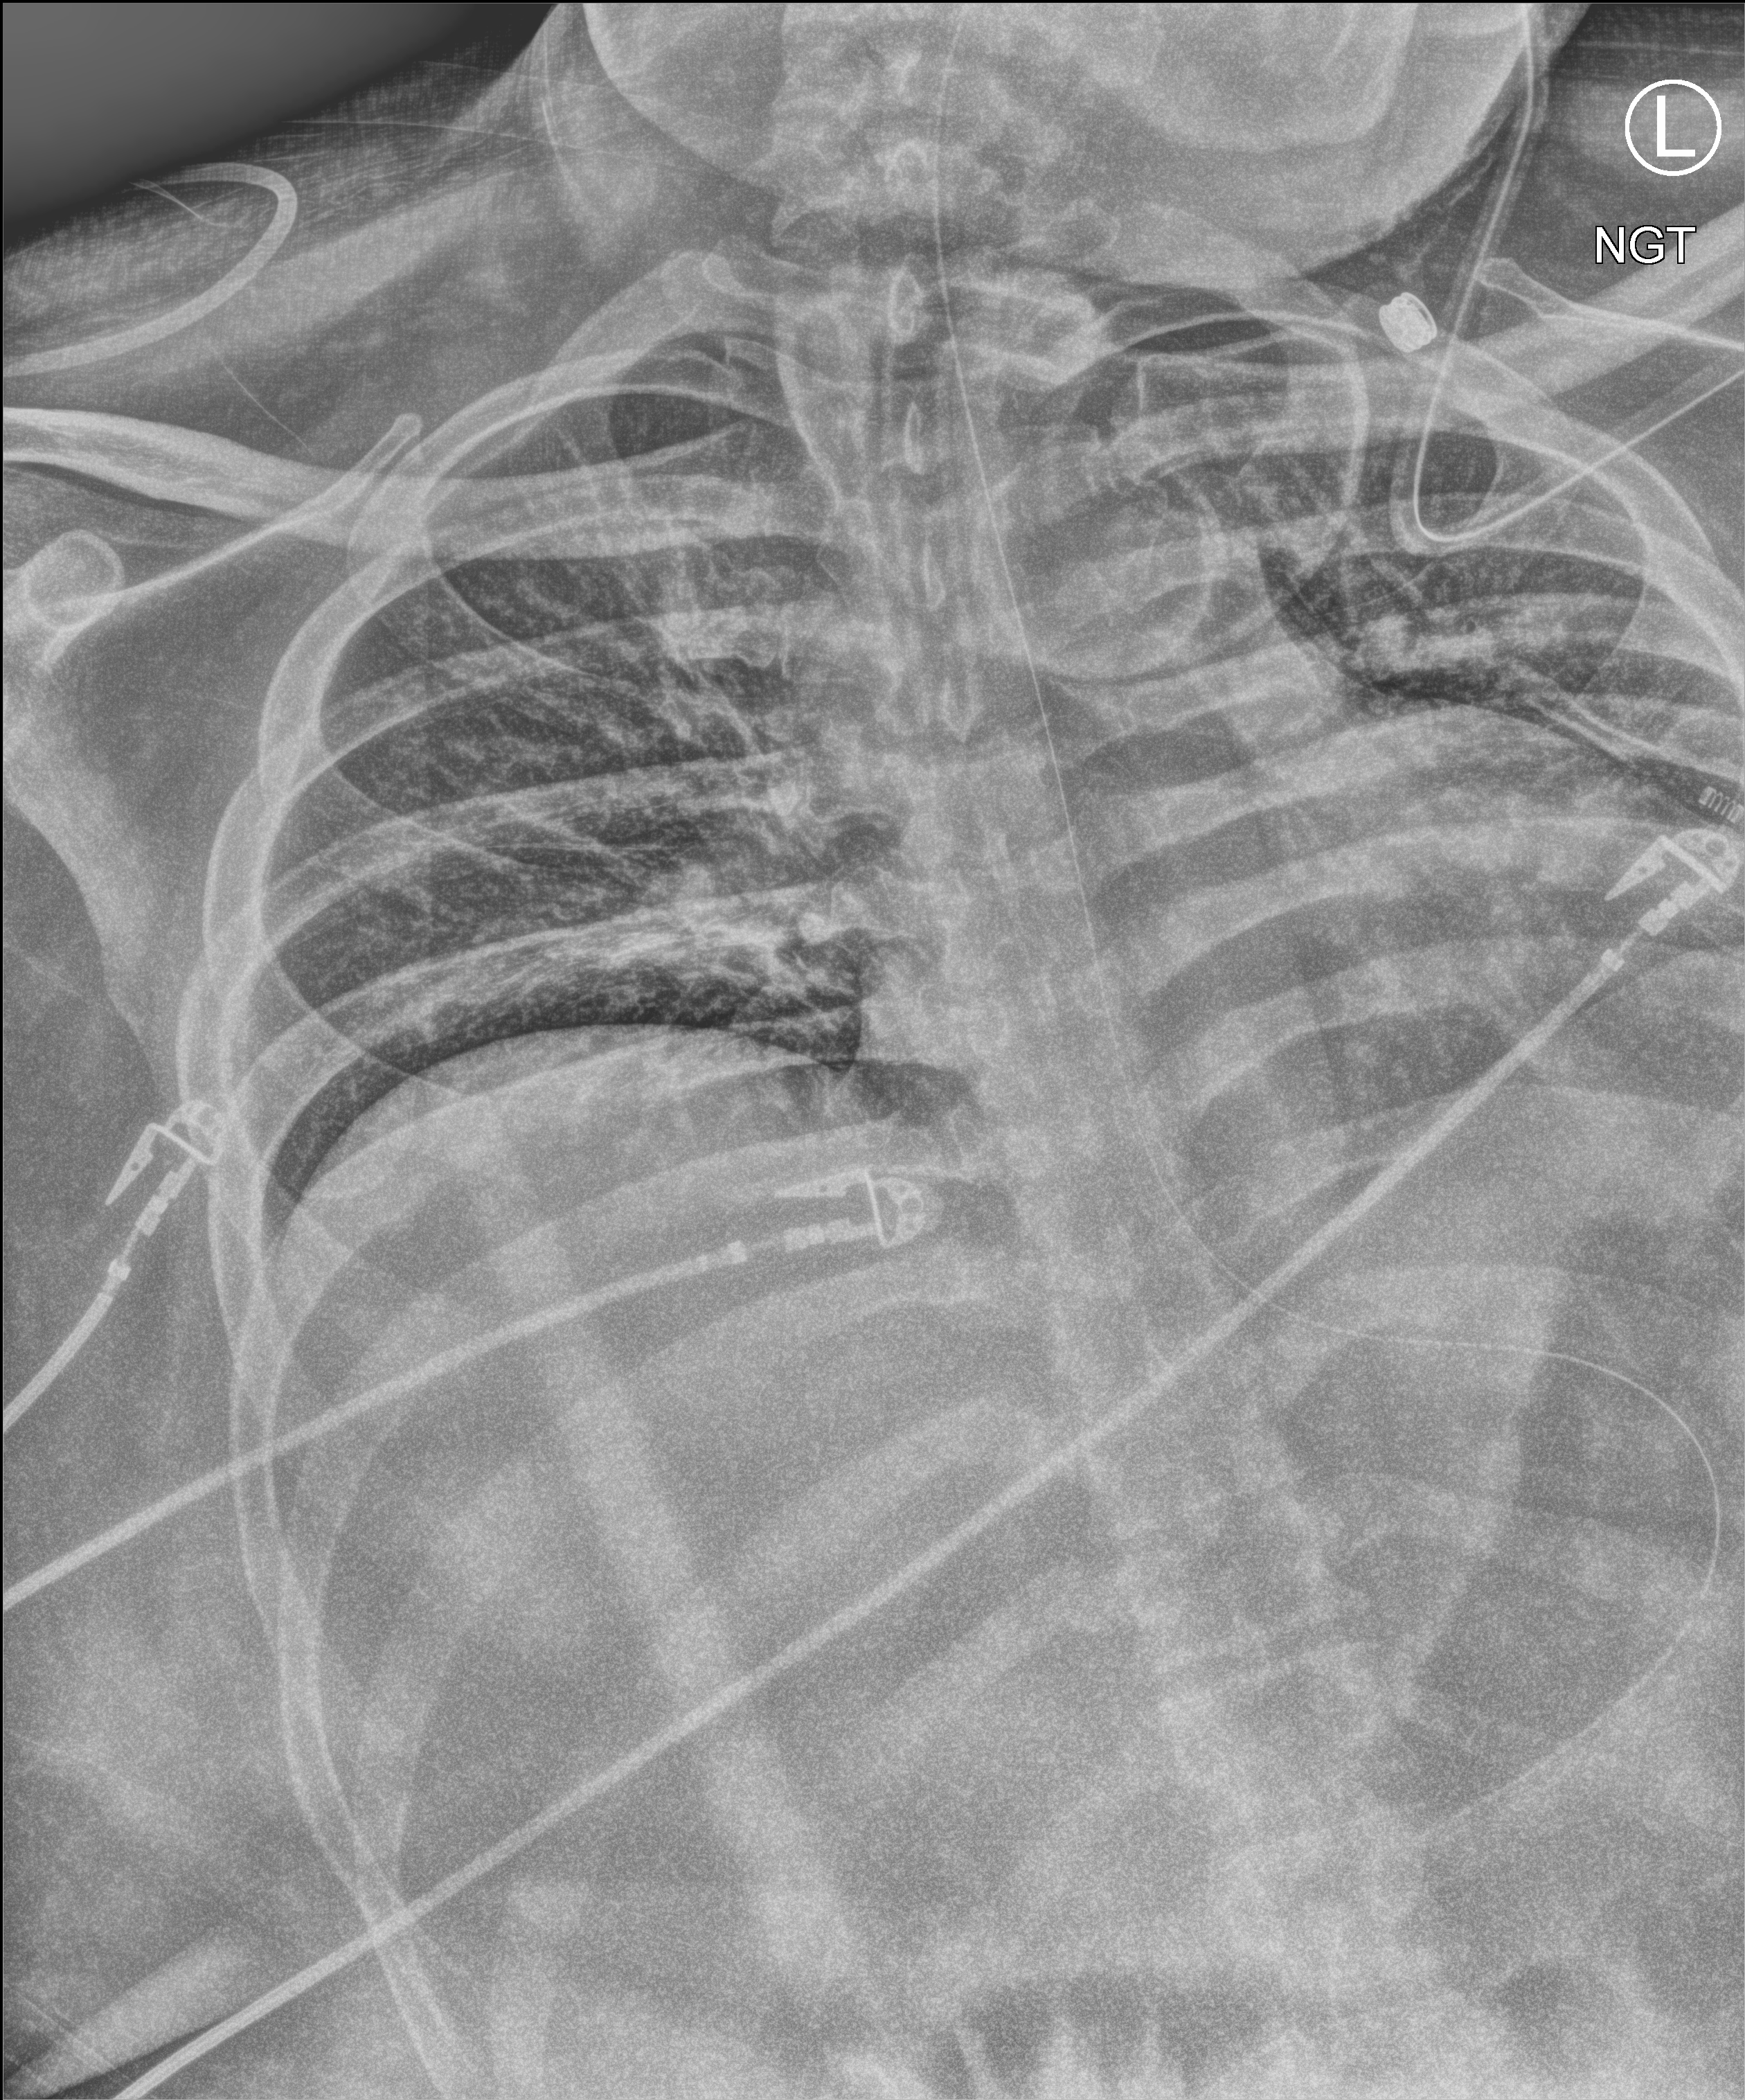
Bedside chest radiograph (computed radiography). Male patient hospitalised with COVID-19, age 18–59 years.
From the hospital-stay record, not from the radiograph (when in the stay this image was taken is not recorded): admitted to intensive care during this hospital stay: yes; chronic kidney disease (admission record): no.